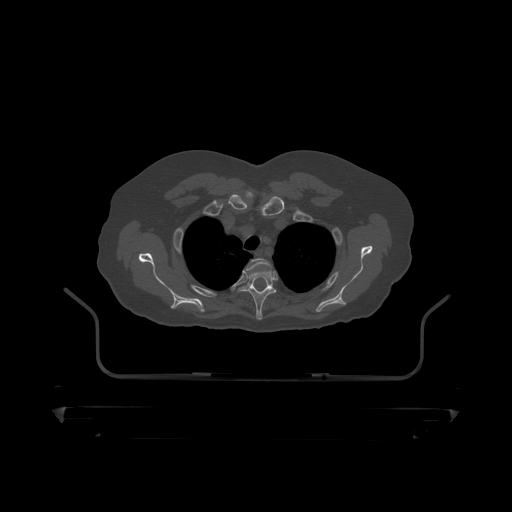
CT including the spine, one axial slice. Slice 359 of 390 in the series (ordered by position). Reconstruction kernel STANDARD. Bone window (W 1800 / L 400 HU). 512 × 512 image matrix, field of view 650 × 650 mm. Male patient, age 60 years. From the clinical record (not read from this slice): primary cancer: prostate.
Annotated regions visible in this slice (semi-automatically segmented with operator editing):
- T2 vertebra: box from (x=246, y=259) to (x=269, y=271) px
- T3 vertebra: (x=238, y=265)–(x=280, y=319)